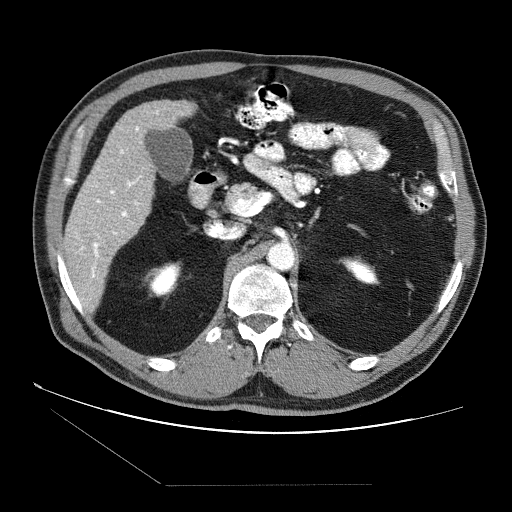
Contrast-enhanced abdominal CT (liver protocol), one axial slice. Position 32 of 87 along the scan axis. Reconstruction kernel STANDARD. 120 kVp. Soft-tissue window (W 400 / L 40 HU). 2.5 mm slice thickness. 512 × 512 image matrix, field of view 400 × 400 mm. From the clinical record (not read from this slice): diagnosis: hepatocellular carcinoma (patient treated with transarterial chemoembolisation; whether this scan precedes or follows treatment is not stated here); TNM stage (as recorded): Stage-II; Child-Pugh class: B; tumour differentiation: no biopsy; tumour nodularity: multinodular.
Annotated regions visible in this slice (semi-automatic segmentation, software-assisted and operator-edited):
- liver parenchyma outside the tumour (the mass and vessels are separate outlines, so this box may not span the whole liver): bounding box <64,100,194,292> (left, top, right, bottom; pixels)
- liver vessels: <75,111,159,278>